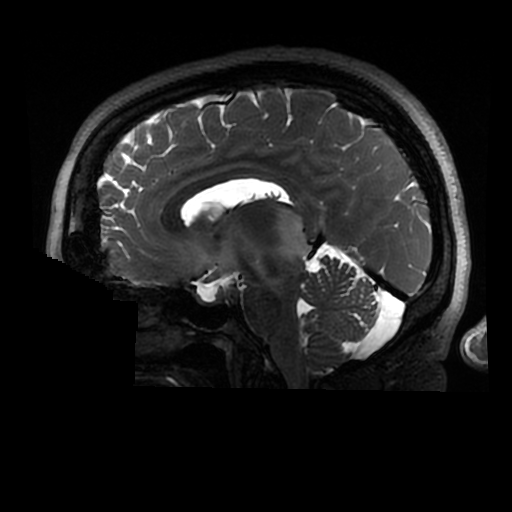
Brain MRI from a brain-tumour surgery series, one sagittal slice; slice 160 of 320 in the series (ordered by position); 0.6 mm slice thickness; 512 × 512 image matrix, field of view 240 × 240 mm. From the clinical record (not read from this slice): histopathology: Astrocytoma; WHO grade: 2; IDH mutation: yes.
Structures marked on this image (outlined manually by an expert reader):
- tumour: bounding box [x1, y1, x2, y2] px = [273, 205, 307, 263]